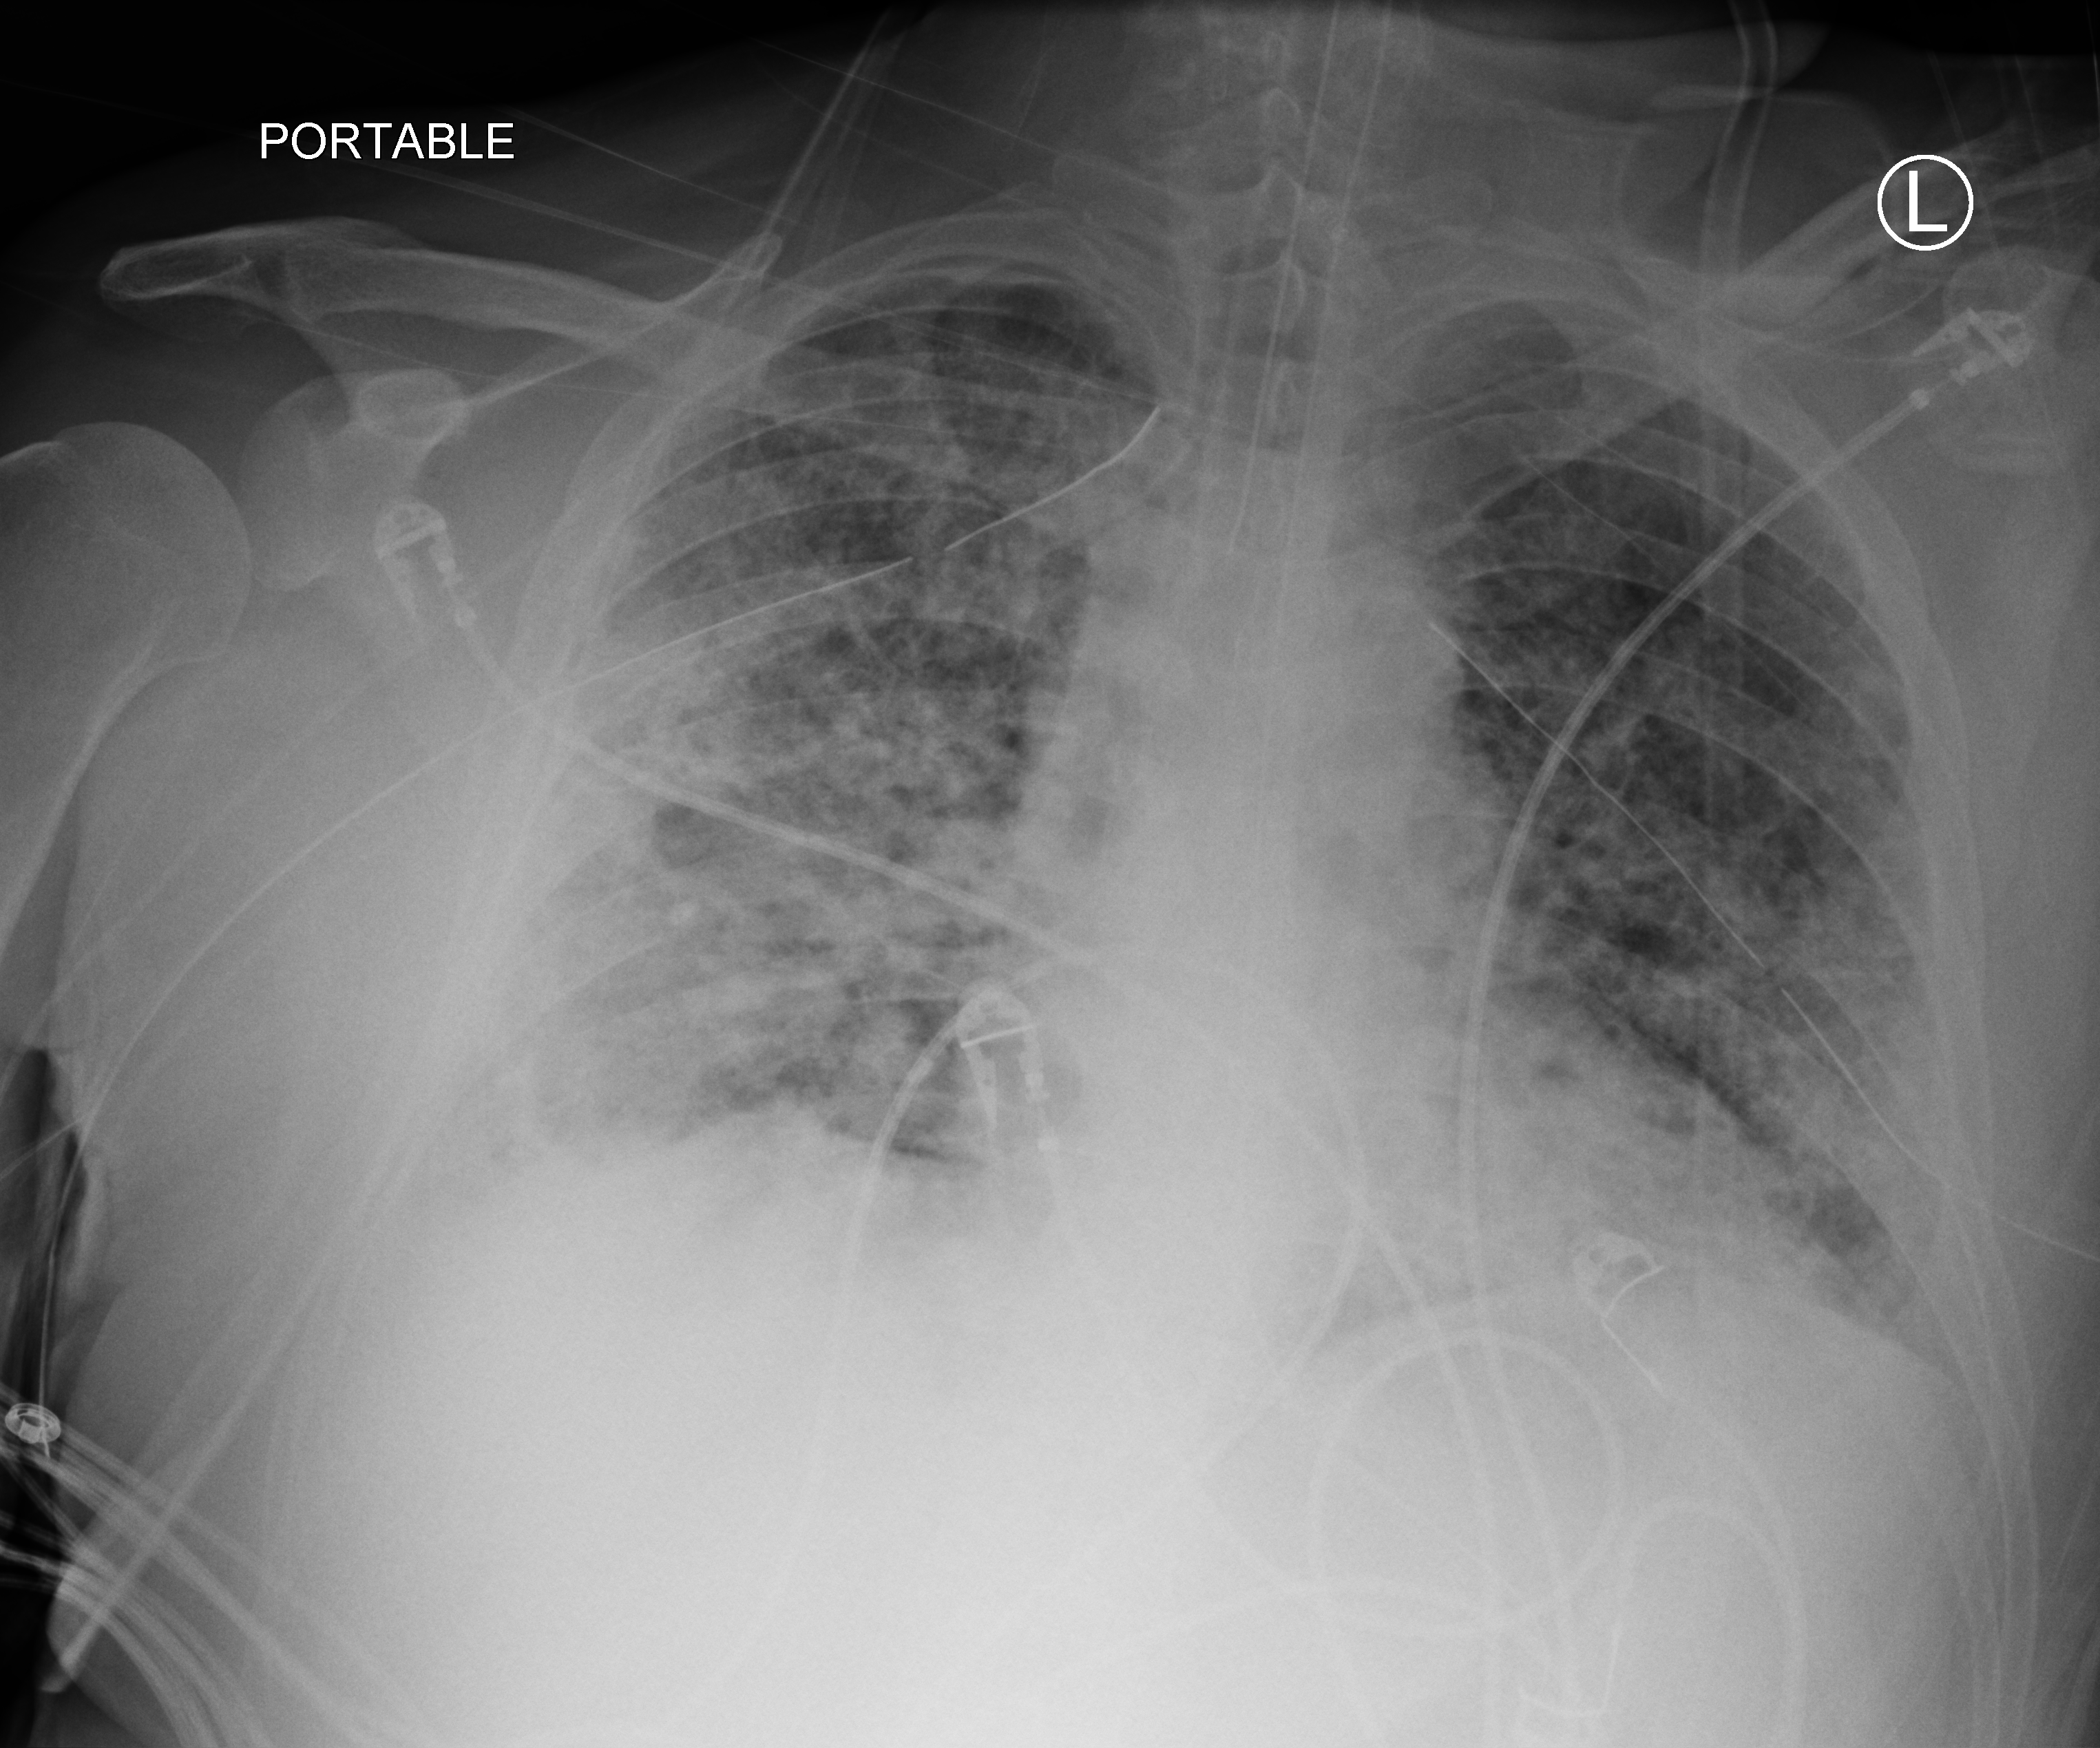
Bedside chest radiograph (computed radiography), anteroposterior (AP) projection. Patient hospitalised with COVID-19; male, aged 18–59 years.
Hospital-stay facts (about this admission, not read from this image; timing relative to this image not recorded):
- mechanically ventilated during this hospital stay: yes
- admitted to intensive care during this hospital stay: yes